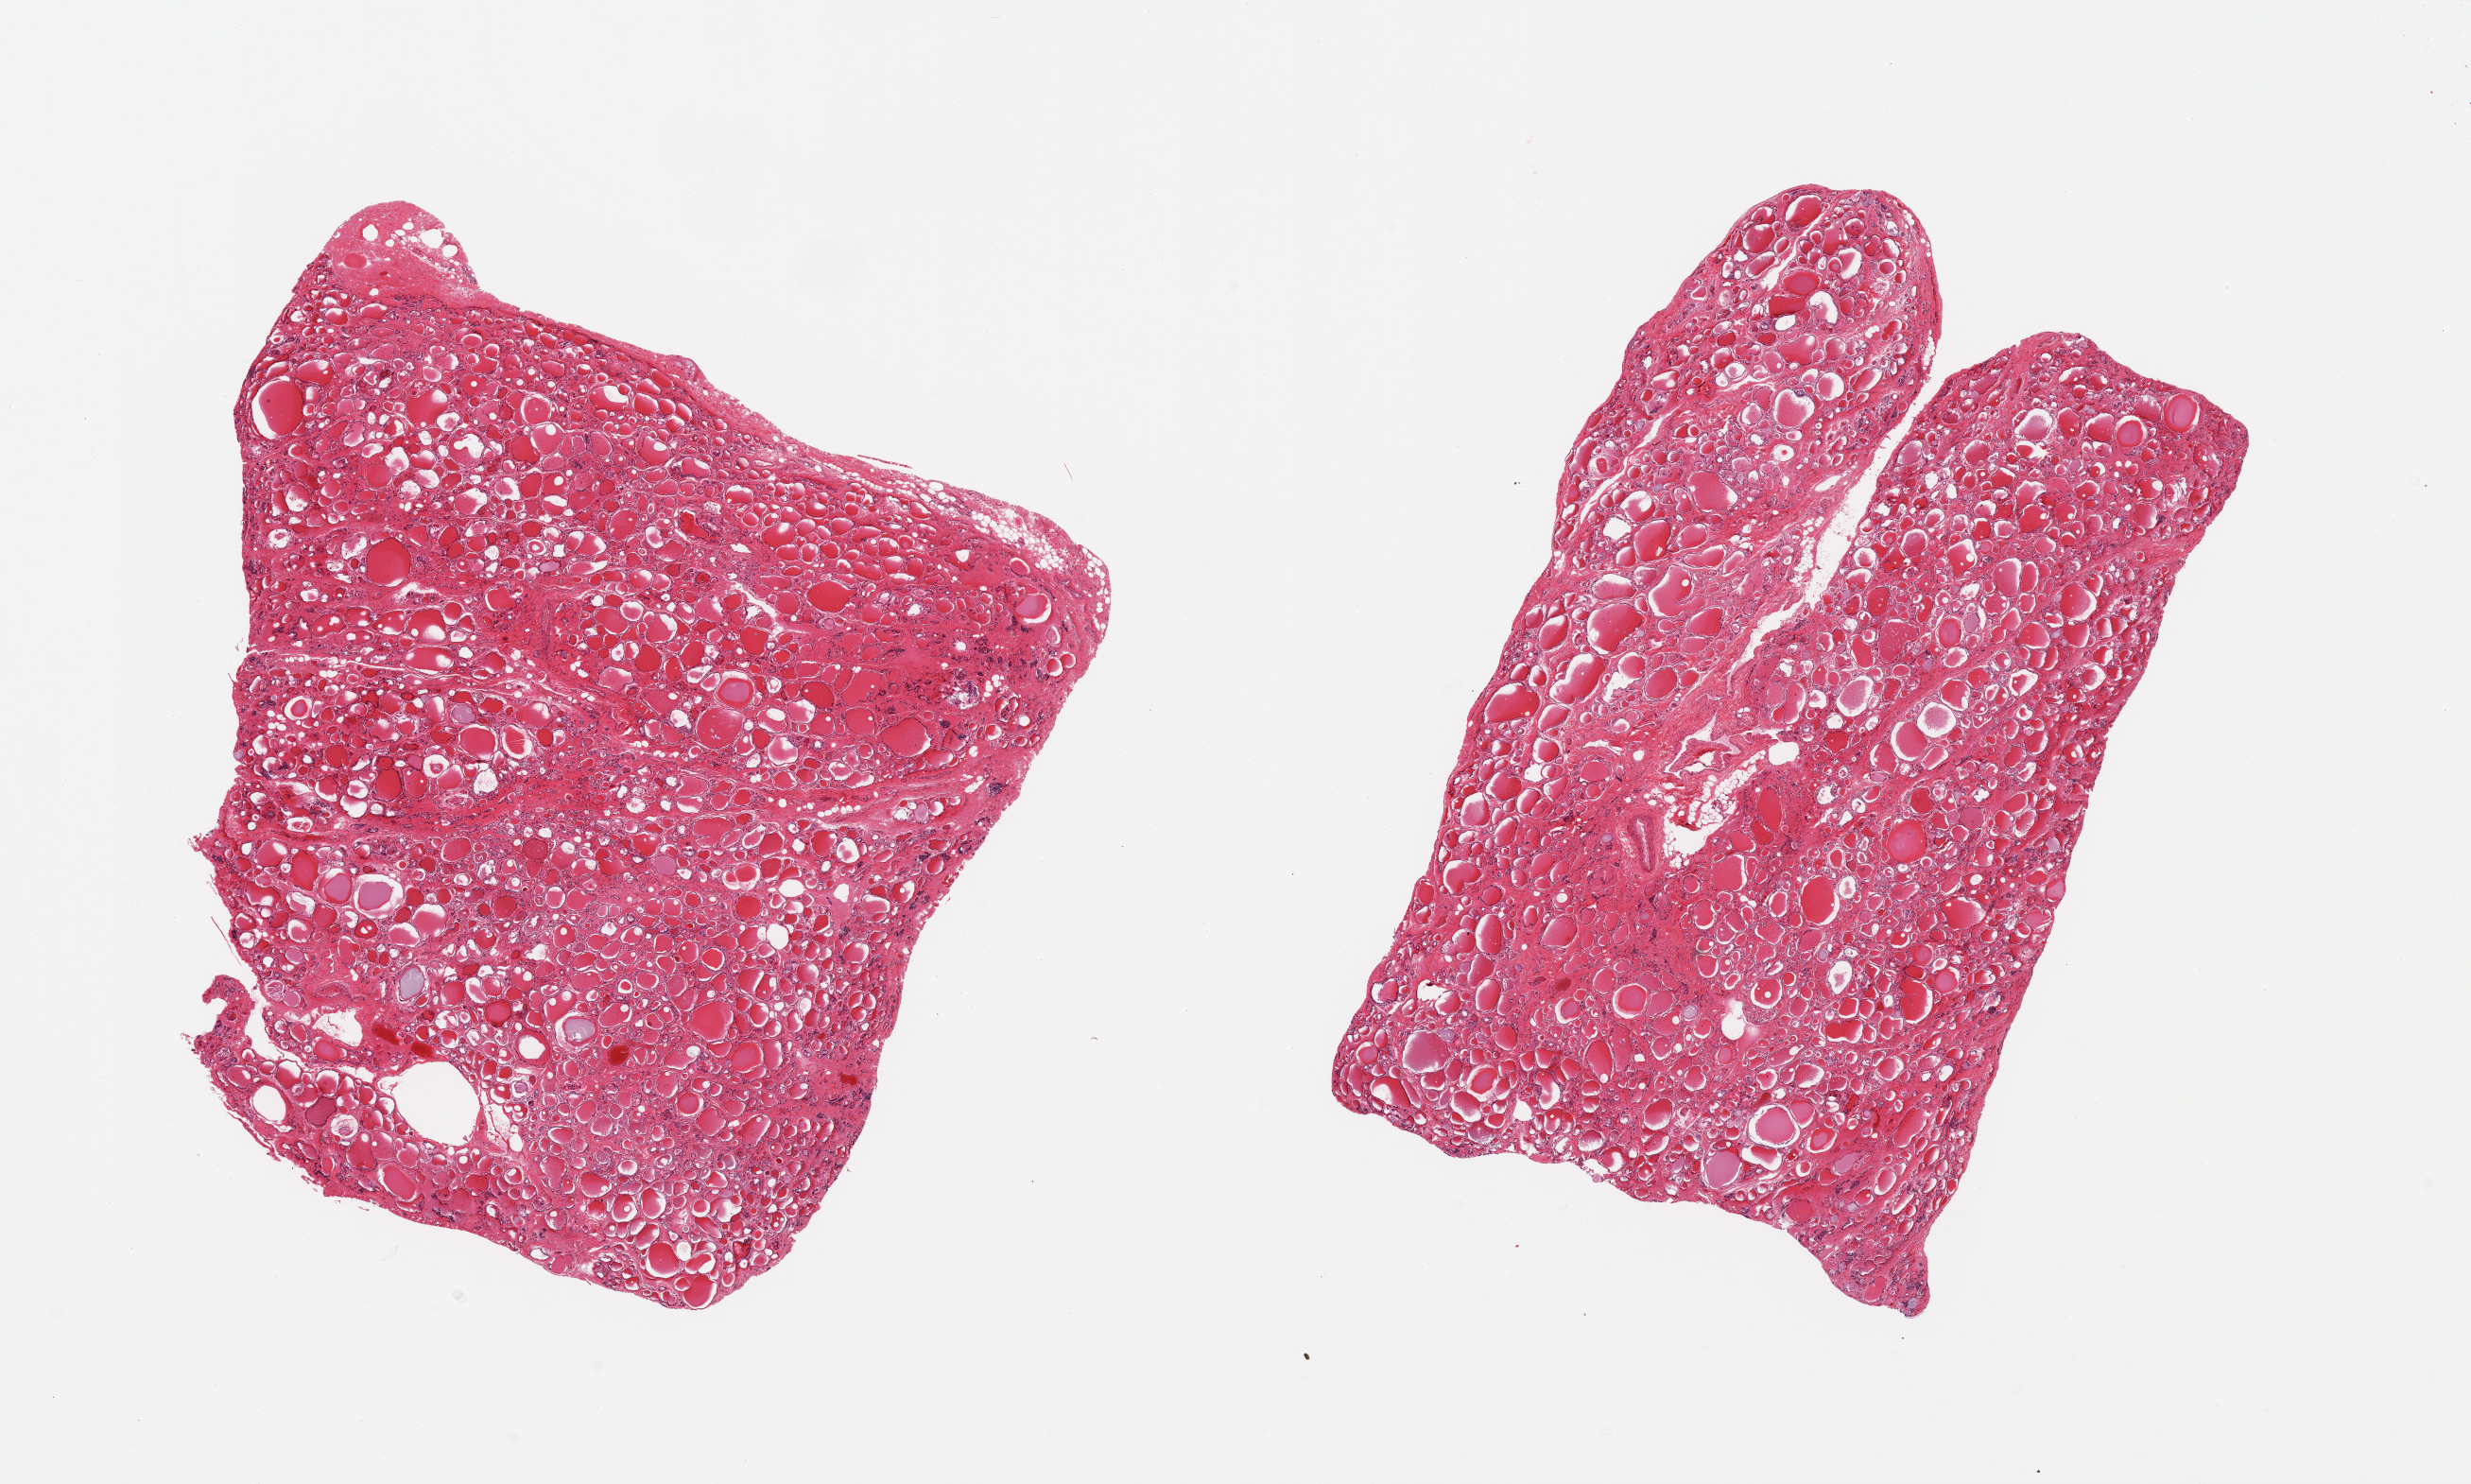
H&E whole-slide image, a low-resolution overview of the entire scanned area, about 20.7 x 12.4 mm. PAXgene-fixed, paraffin-embedded tissue. Sampled site (target tissue): thyroid. Donor tissue sample. Donor sex: female.
Reviewer comment on this tissue sample: 2 pieces, no abnormalities.